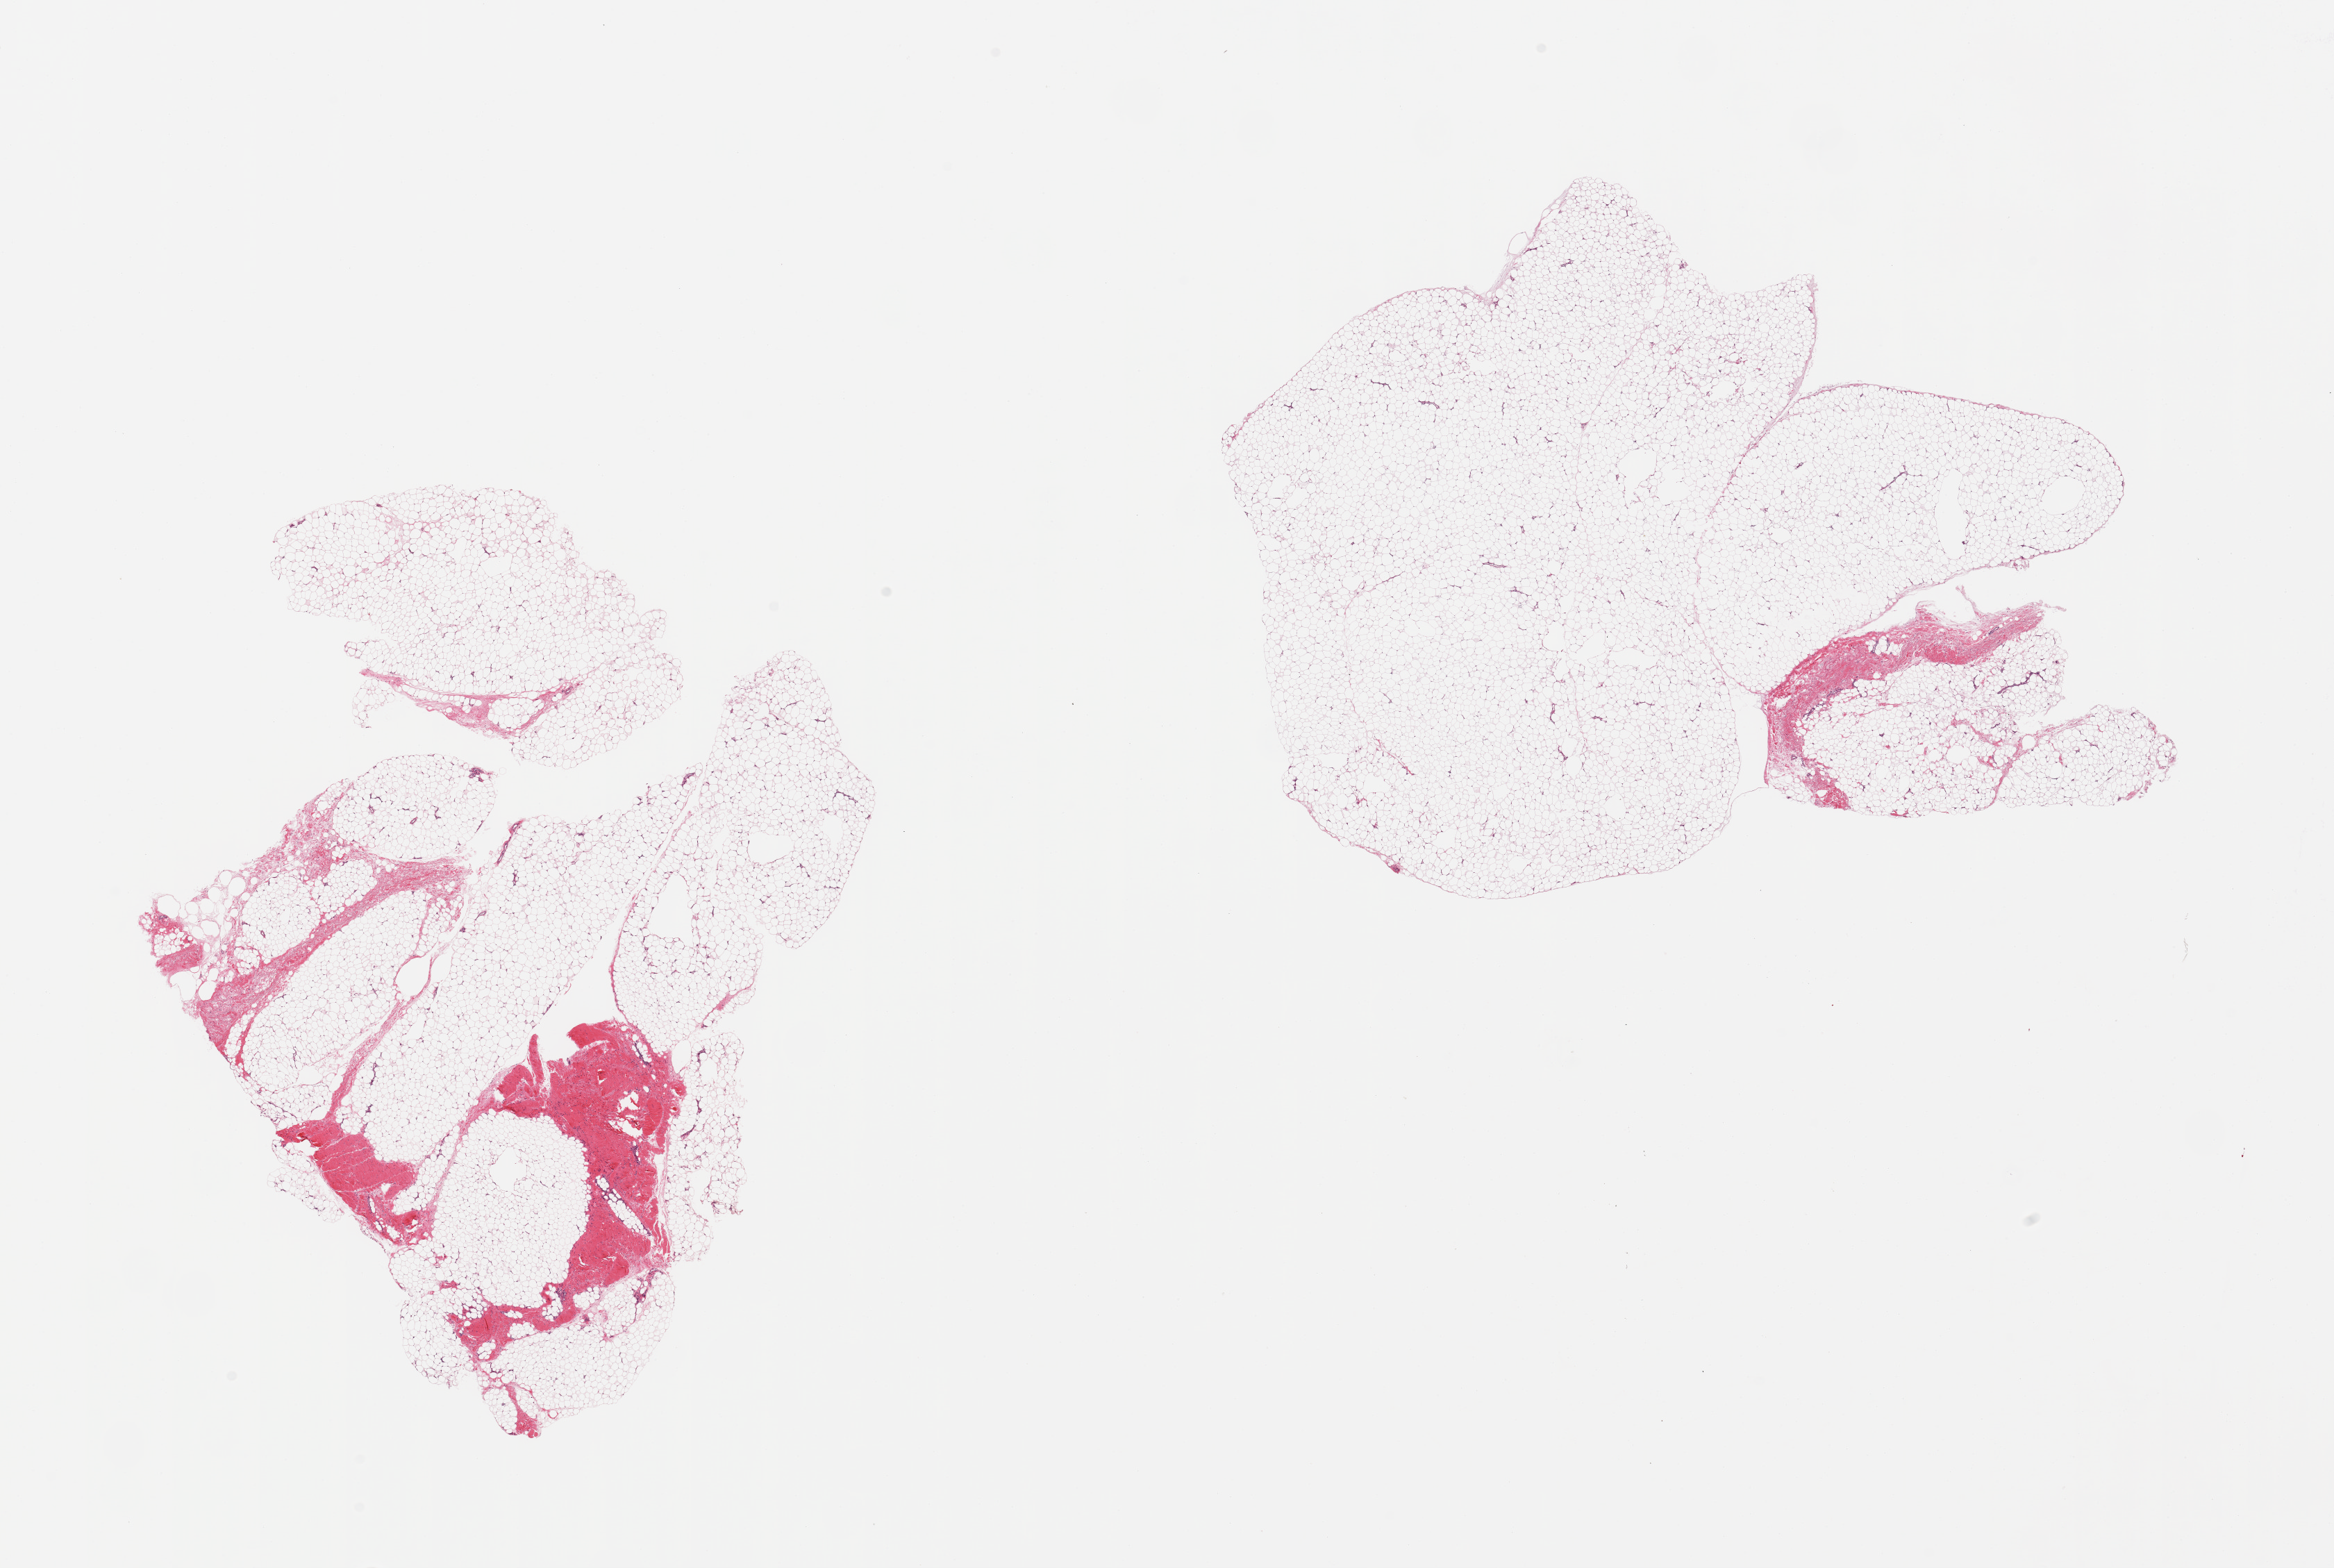
Whole-slide image, haematoxylin and eosin stain, shown as a low-resolution overview of the whole scanned area (about 26.6 x 17.9 mm), PAXgene-fixed paraffin-embedded (PFPE) section, section of adipose tissue (target tissue), tissue donor sample. Male donor.
Review note (as recorded): 2 pieces; fat with 20% and 10% fibrous tissue/tendon.